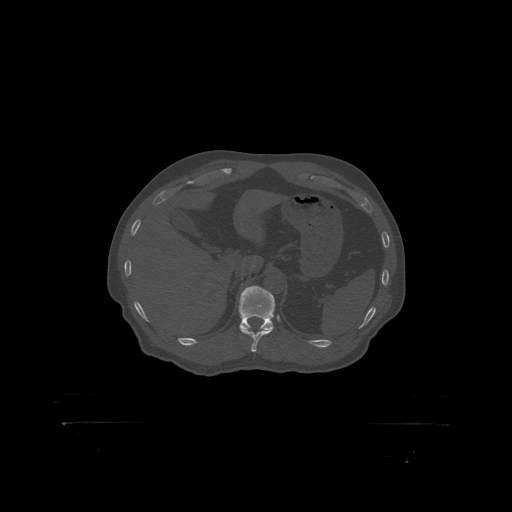
CT including the spine, one axial slice. Position 366 of 399 along the scan axis. Reconstruction kernel STANDARD. Bone window (W 1800 / L 400 HU). 1.25 mm slice thickness. 512 × 512 image matrix. Male patient, age 46 years. From the clinical record (not read from this slice): primary cancer: skin.
Annotated regions visible in this slice (semi-automatic segmentation, software-assisted and operator-edited):
- T12 vertebra: box from (x=239, y=287) to (x=275, y=319) px